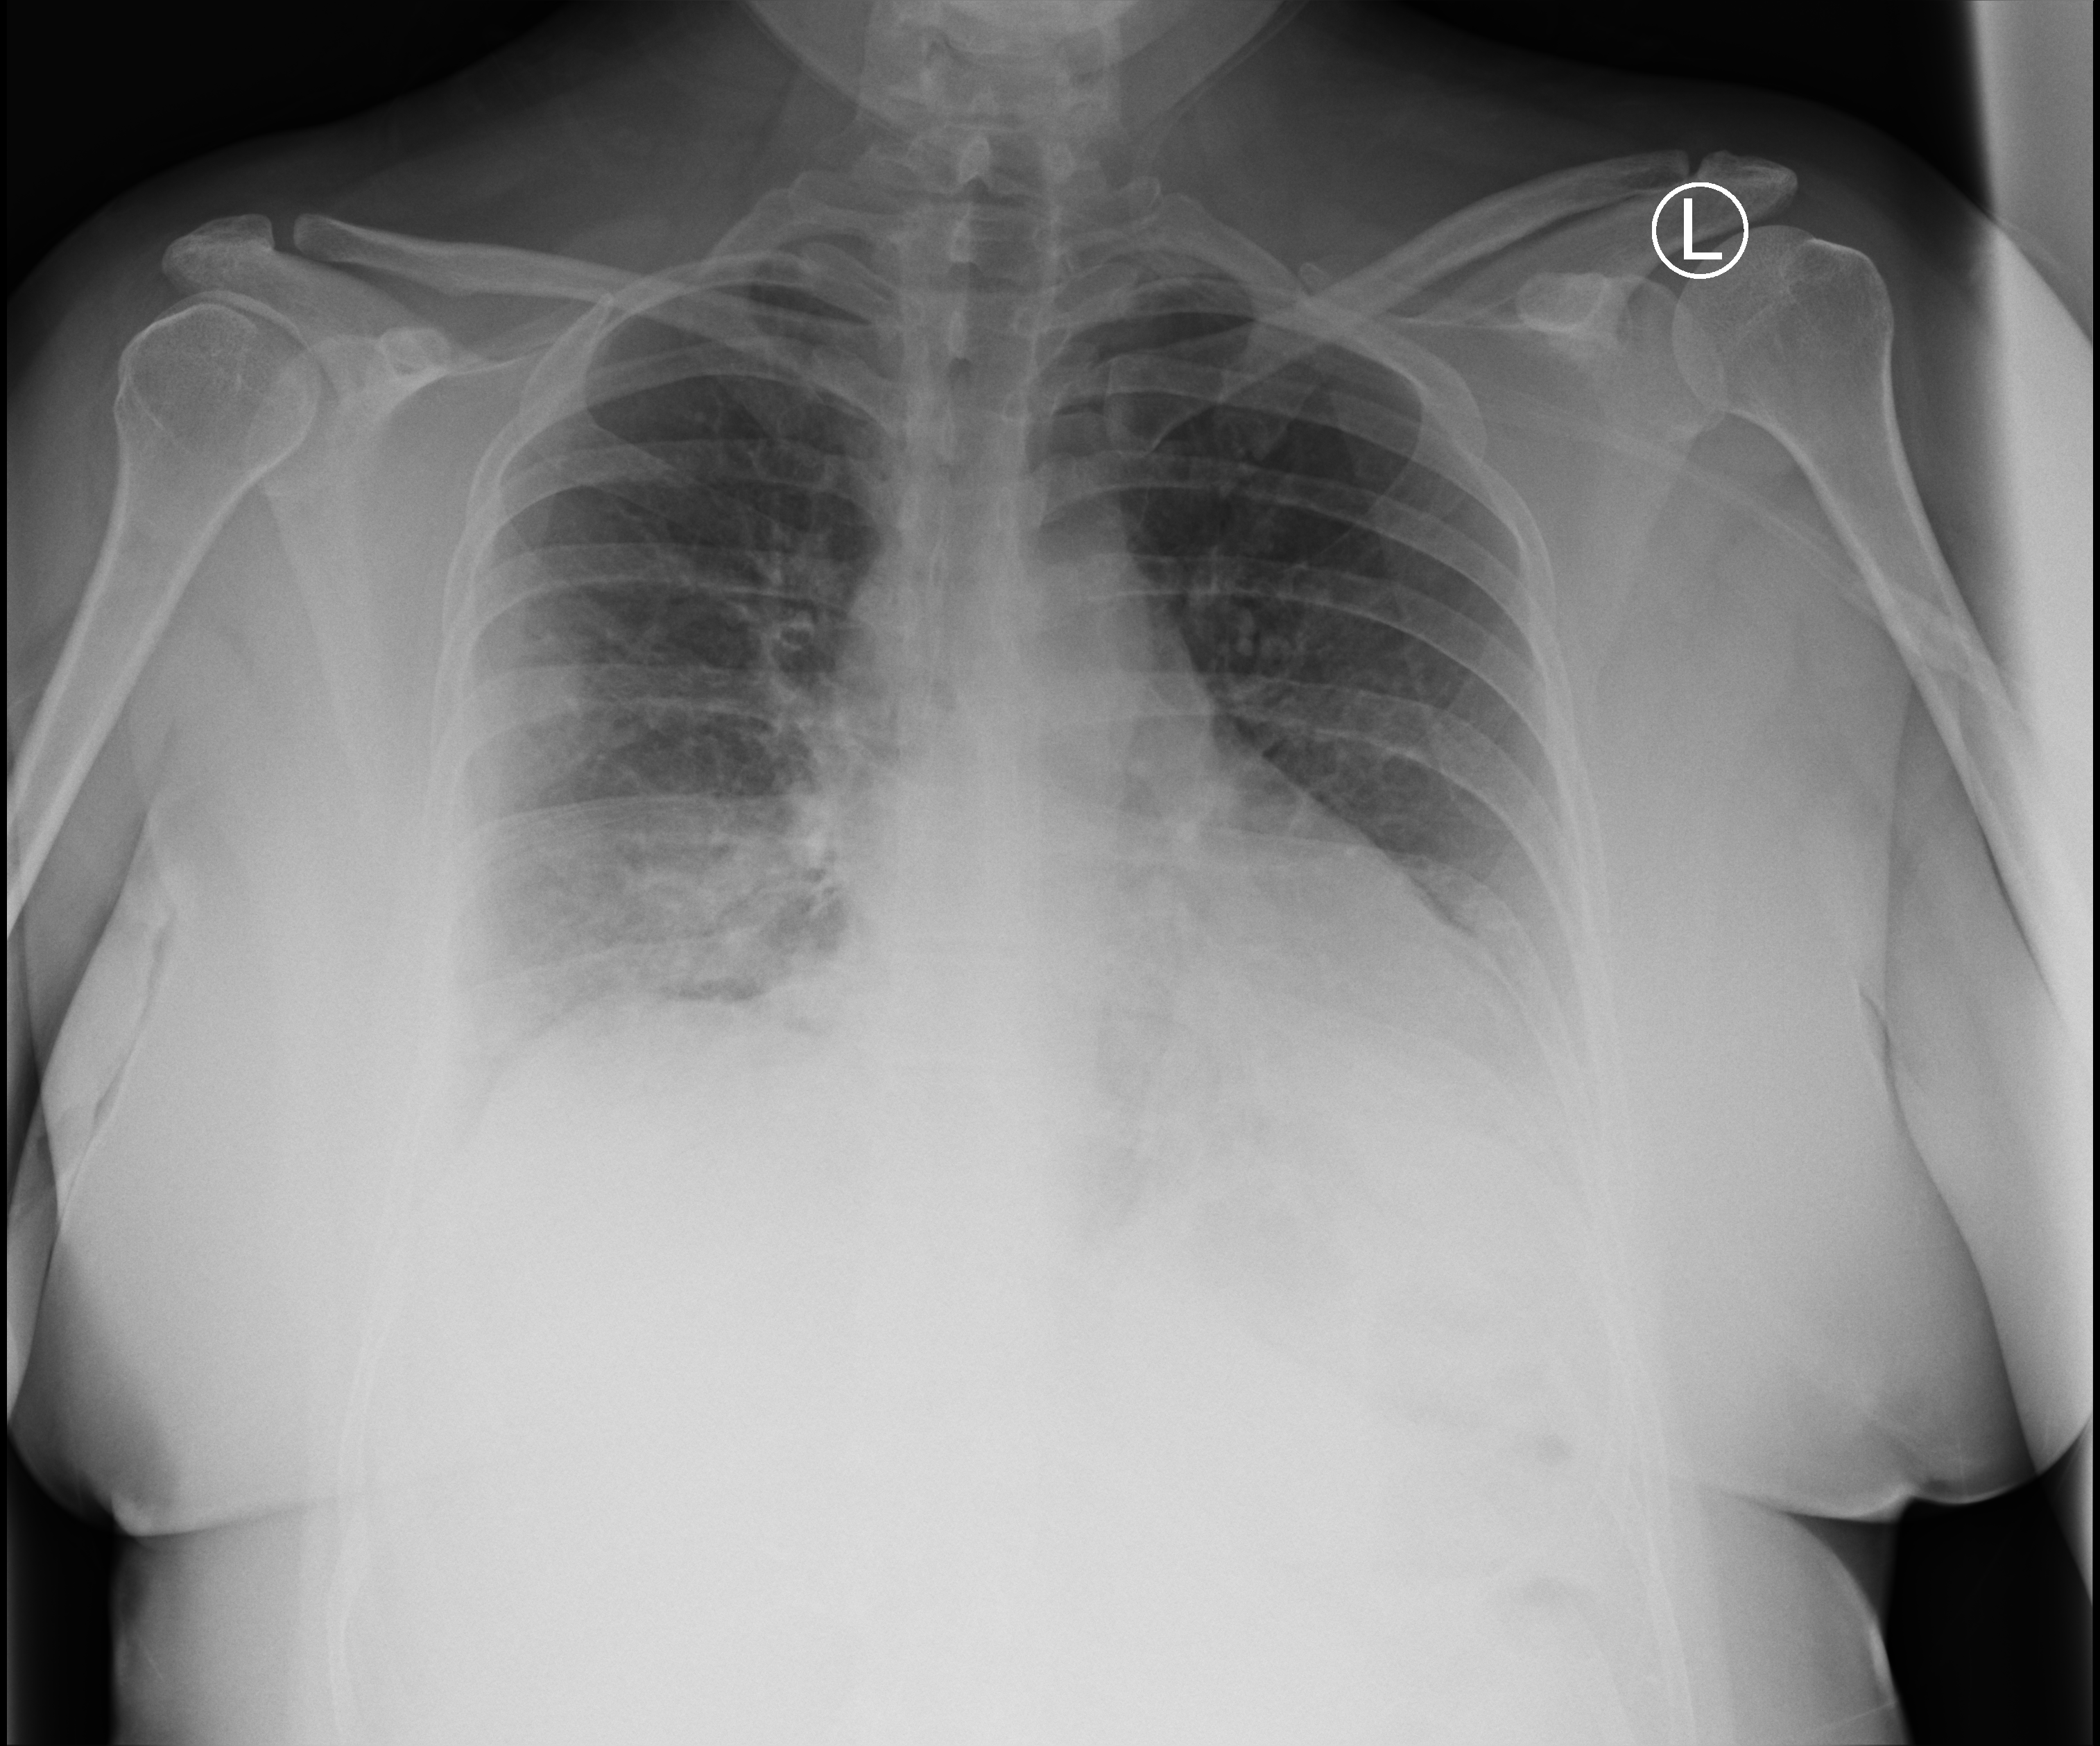
Portable chest radiograph; anteroposterior (AP) projection. Patient hospitalised with COVID-19; female, aged 18–59 years.
From the hospital-stay record, not from the radiograph (when in the stay this image was taken is not recorded): admitted to intensive care during this hospital stay: no.